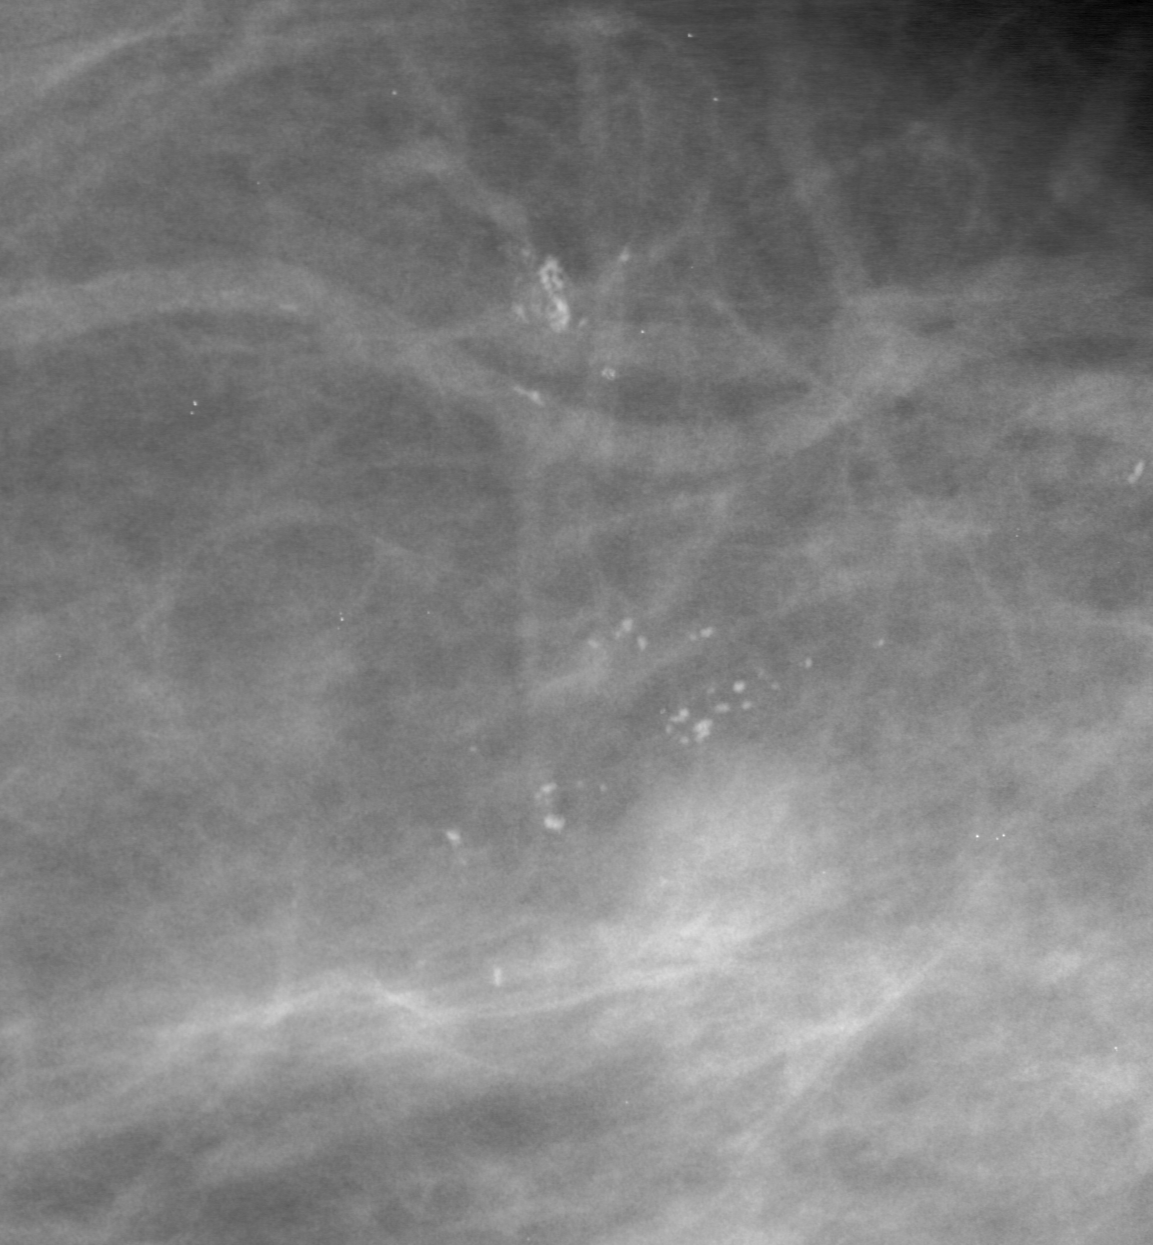
Cropped region of a digitized screen-film mammogram centred on a radiologist-marked abnormality; left breast; CC view; BI-RADS breast density category 2 (scale 1–4).
Finding: calcifications, morphology round and regular / pleomorphic, distribution clustered; BI-RADS assessment category 0 (incomplete: needs additional imaging); pathology result (as recorded, not read from the image): benign.